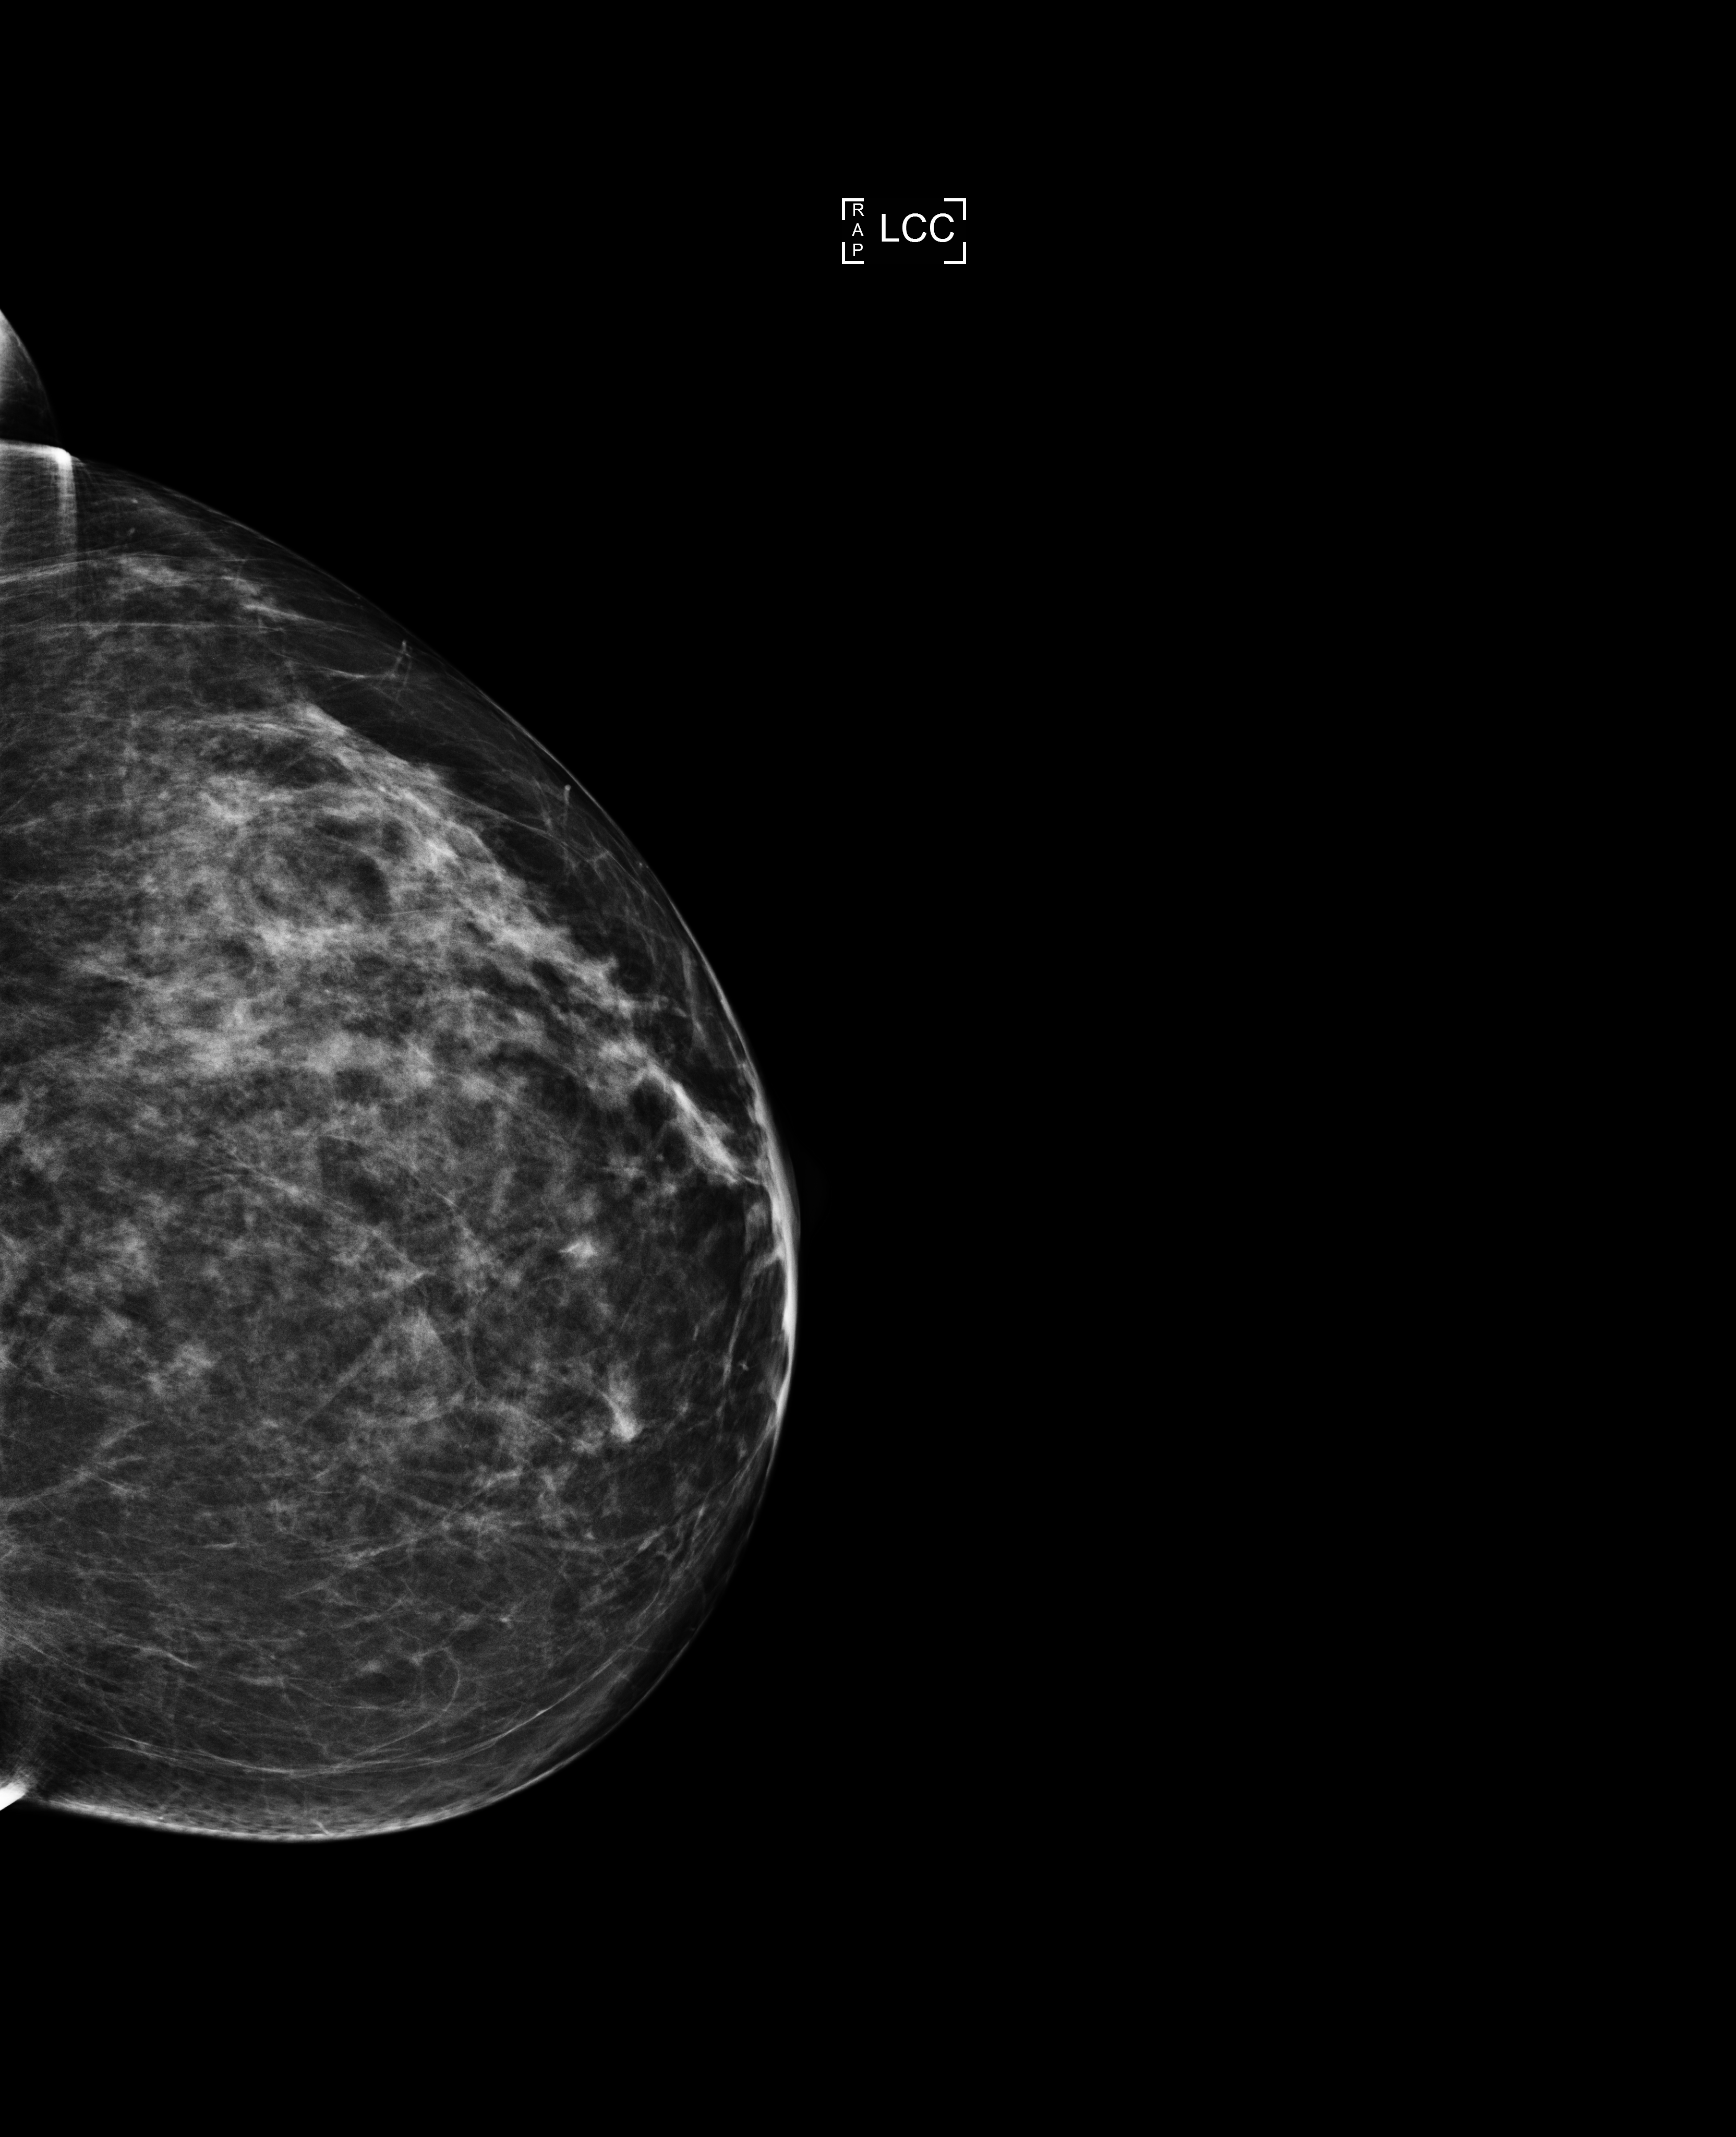
Annual screening mammography examination, compressed breast thickness 62 mm. Patient aged 49 years (female).
Image type: full-field digital mammogram. Breast: left. Projection: CC view.